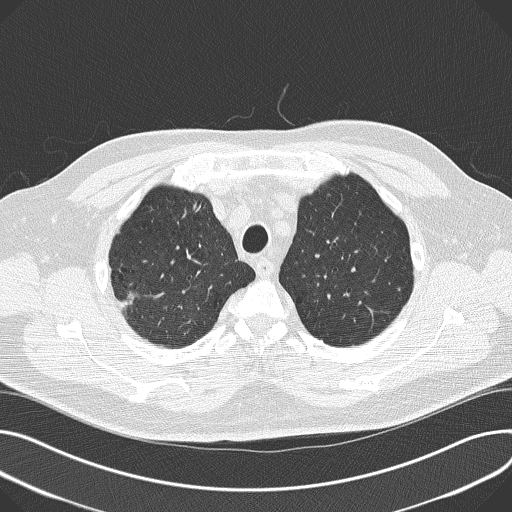
Chest CT (low-dose screening protocol), one axial image; third annual screen; lung window (W 1500 / L -600 HU); lung (sharp) reconstruction kernel (B50f). Male participant, aged 68 years at enrolment.
Lesion marked by an expert reader, bounding box (x1, y1, x2, y2) in pixels: (177, 183, 222, 228). The screening reader recorded 3 non-calcified nodules or masses ≥4 mm on this exam (right upper lobe, left lower lobe, right lower lobe); which of them this box marks is not recorded. Lung cancer was diagnosed 95 days after this screen: combined small cell carcinoma, right upper lobe, undifferentiated (G4), stage IIIB (AJCC 6th edition), 30 mm at pathology.